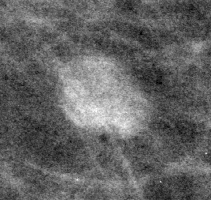
Region of interest cut from a scanned film mammogram (one marked finding), left breast, MLO view, BI-RADS breast density category 1 (scale 1–4).
- Marked abnormality: mass, shape lobulated, margins circumscribed; BI-RADS assessment category 3; subtlety rating 5 on a 1 (subtle) to 5 (obvious) scale; pathology result (as recorded, not read from the image): benign.